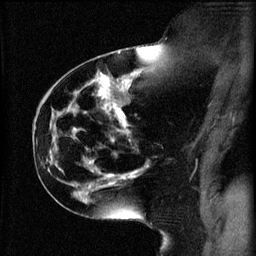
Breast MRI (dynamic contrast-enhanced), one sagittal slice. Slice 32 of 60 in the series (ordered by position). 3 images stored at this slice position (order not interpretable as contrast timing). 1.5 T. TE 4.2 ms, TR 11 ms. 2 mm slice thickness. 256 × 256 image matrix. Patient: female, 44 years.
Structures marked on this image (semi-automatically segmented with operator editing):
- analysis volume of interest (the breast-tissue region the enhancement analysis was run in; not a lesion): bounding box [x1, y1, x2, y2] px = [110, 124, 151, 179]
- tumour enhancement mask (voxels above the 70 % enhancement threshold inside the analysis volume of interest): [110, 124, 143, 179]